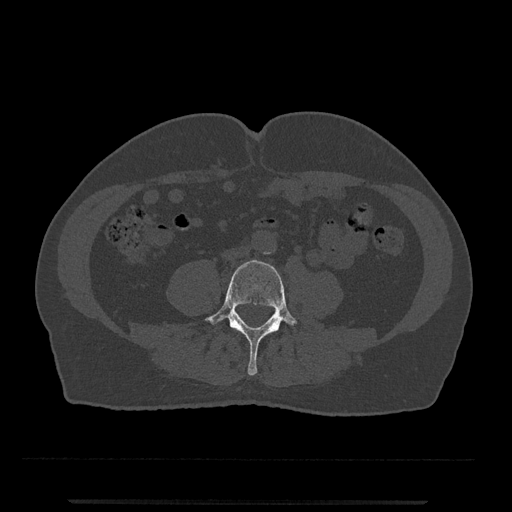
CT including the spine, one axial slice; slice 139 of 797 in the series (ordered by position); 120 kVp; bone window (W 1800 / L 400 HU); 512 × 512 image matrix, field of view 419 × 419 mm. Male patient, age 63 years. Case-level facts recorded for this patient, not image findings: primary cancer: prostate.
Structures marked on this image (semi-automatic segmentation, software-assisted and operator-edited):
- L4 vertebra: bounding box [x1, y1, x2, y2] px = [204, 260, 298, 375]